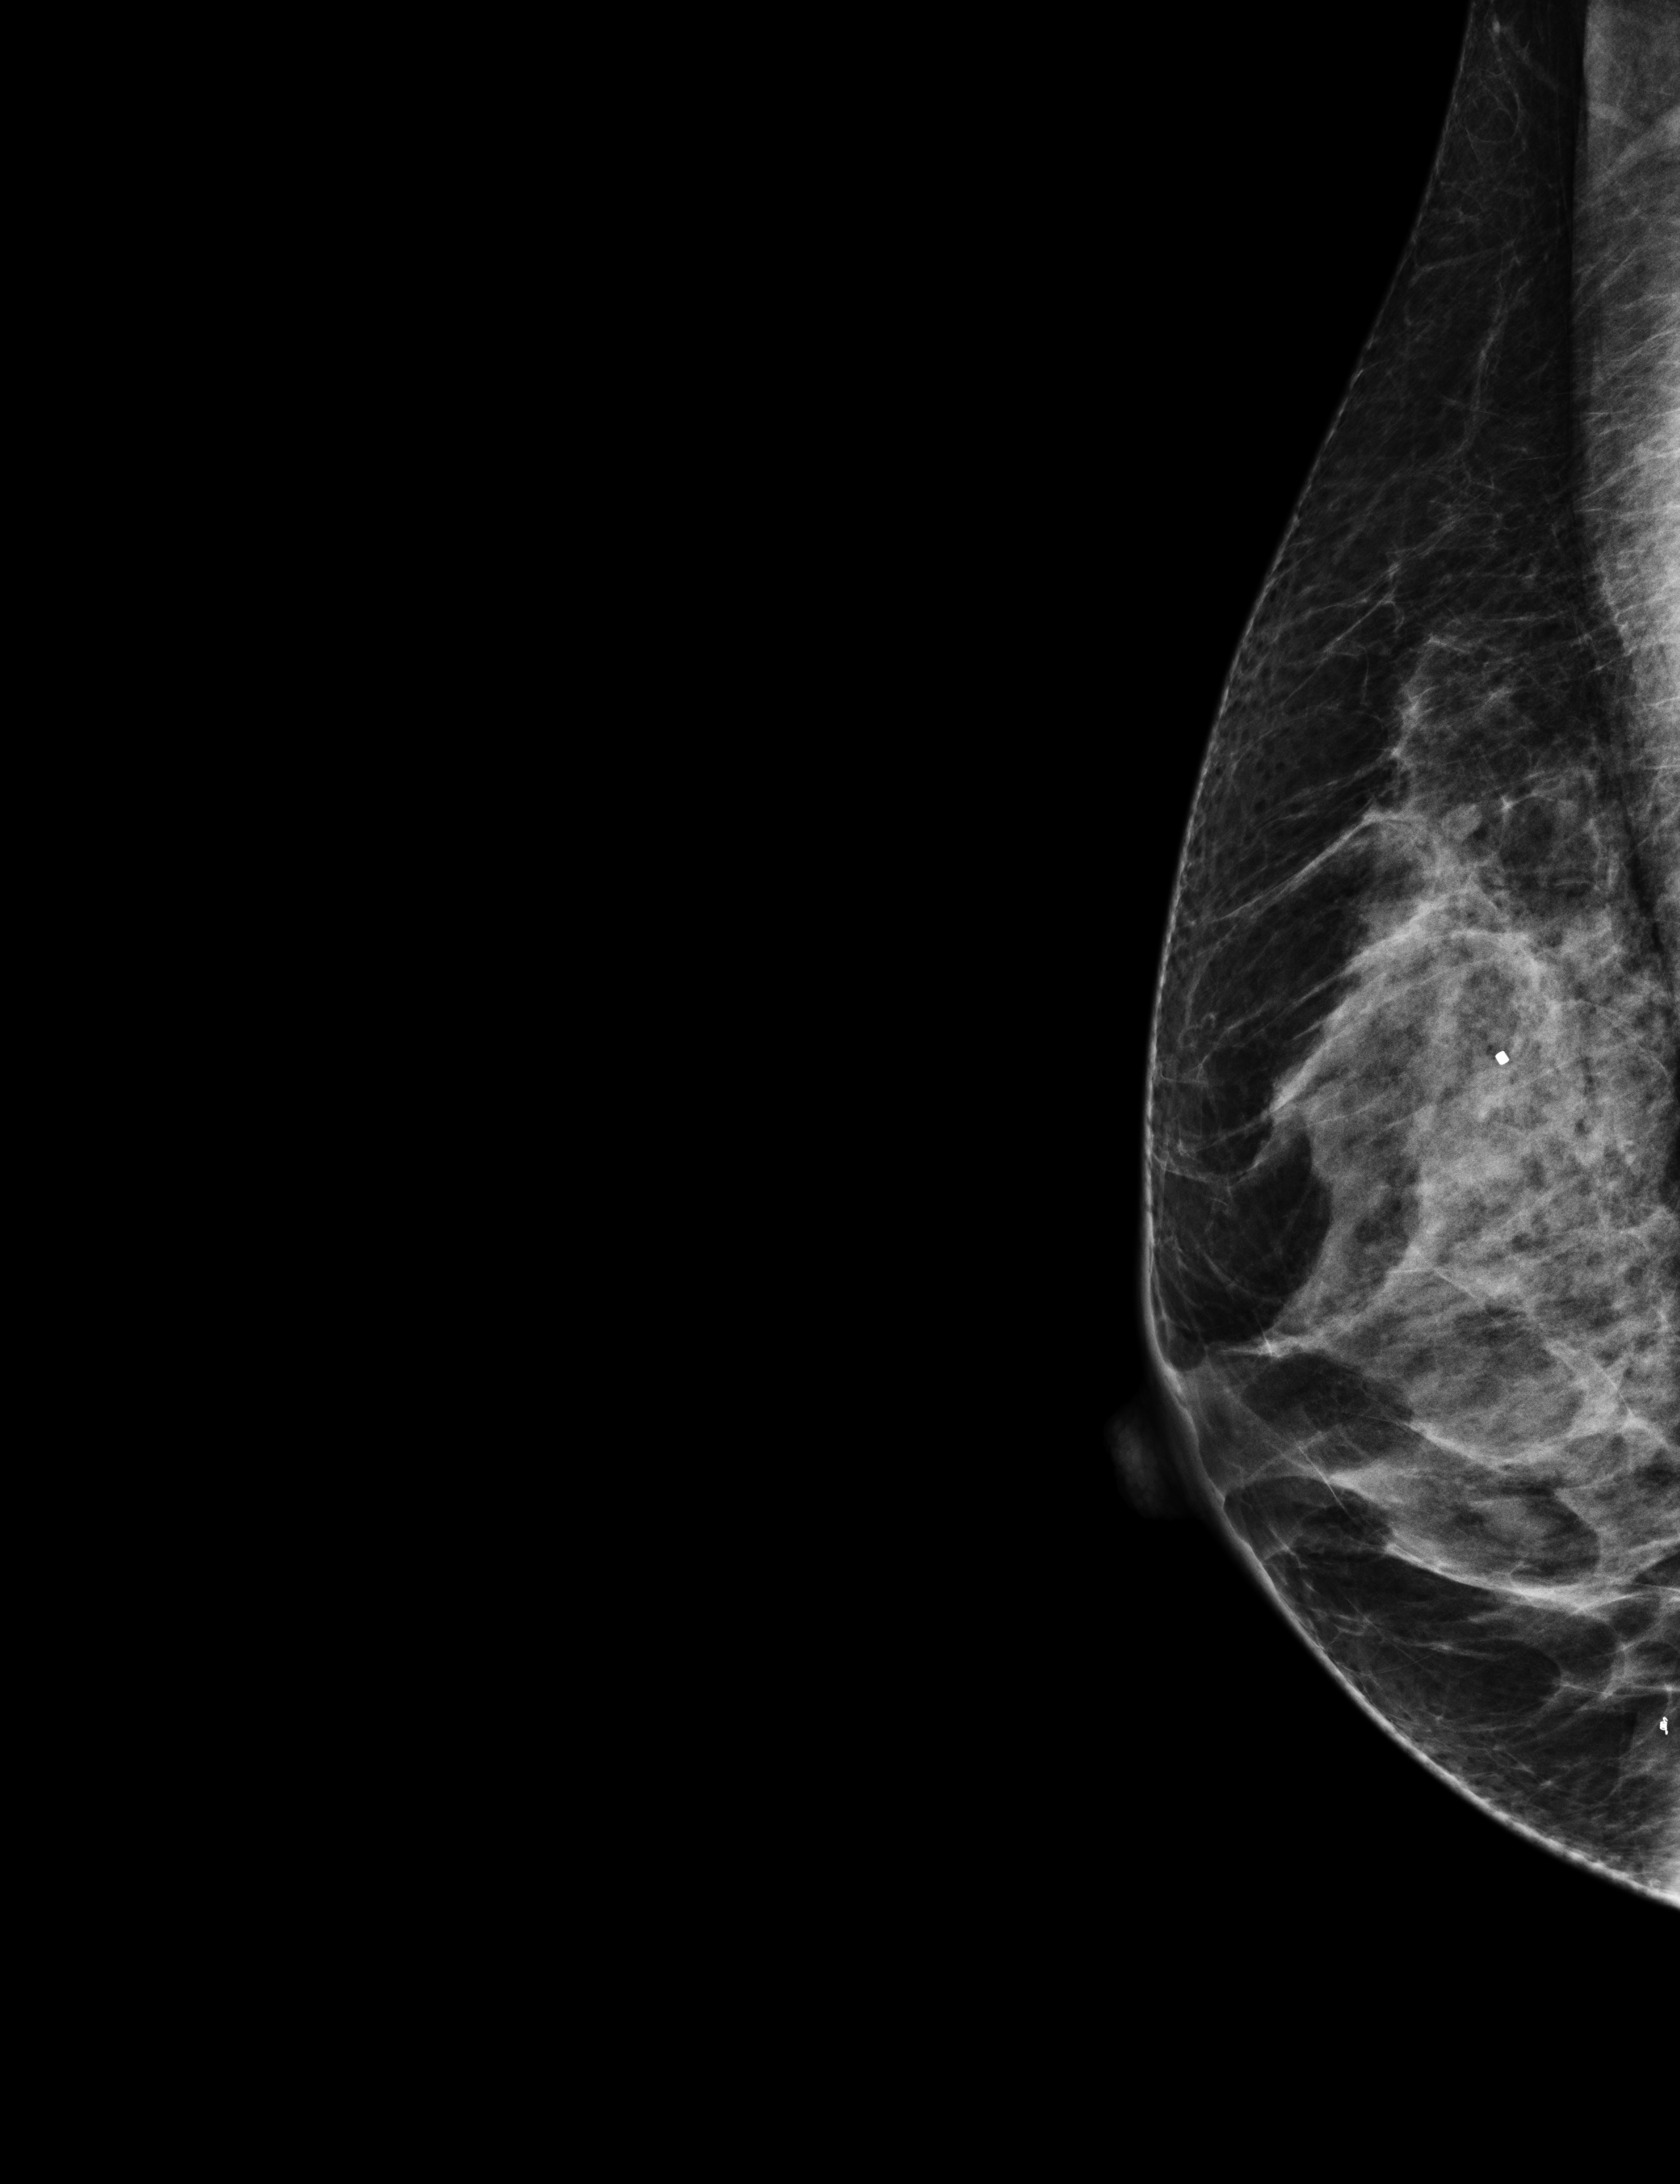
Annual screening mammography examination. Female patient, age 44 years.
Image type: full-field digital mammogram. Breast: right. Projection: exaggerated CC view (lateral).